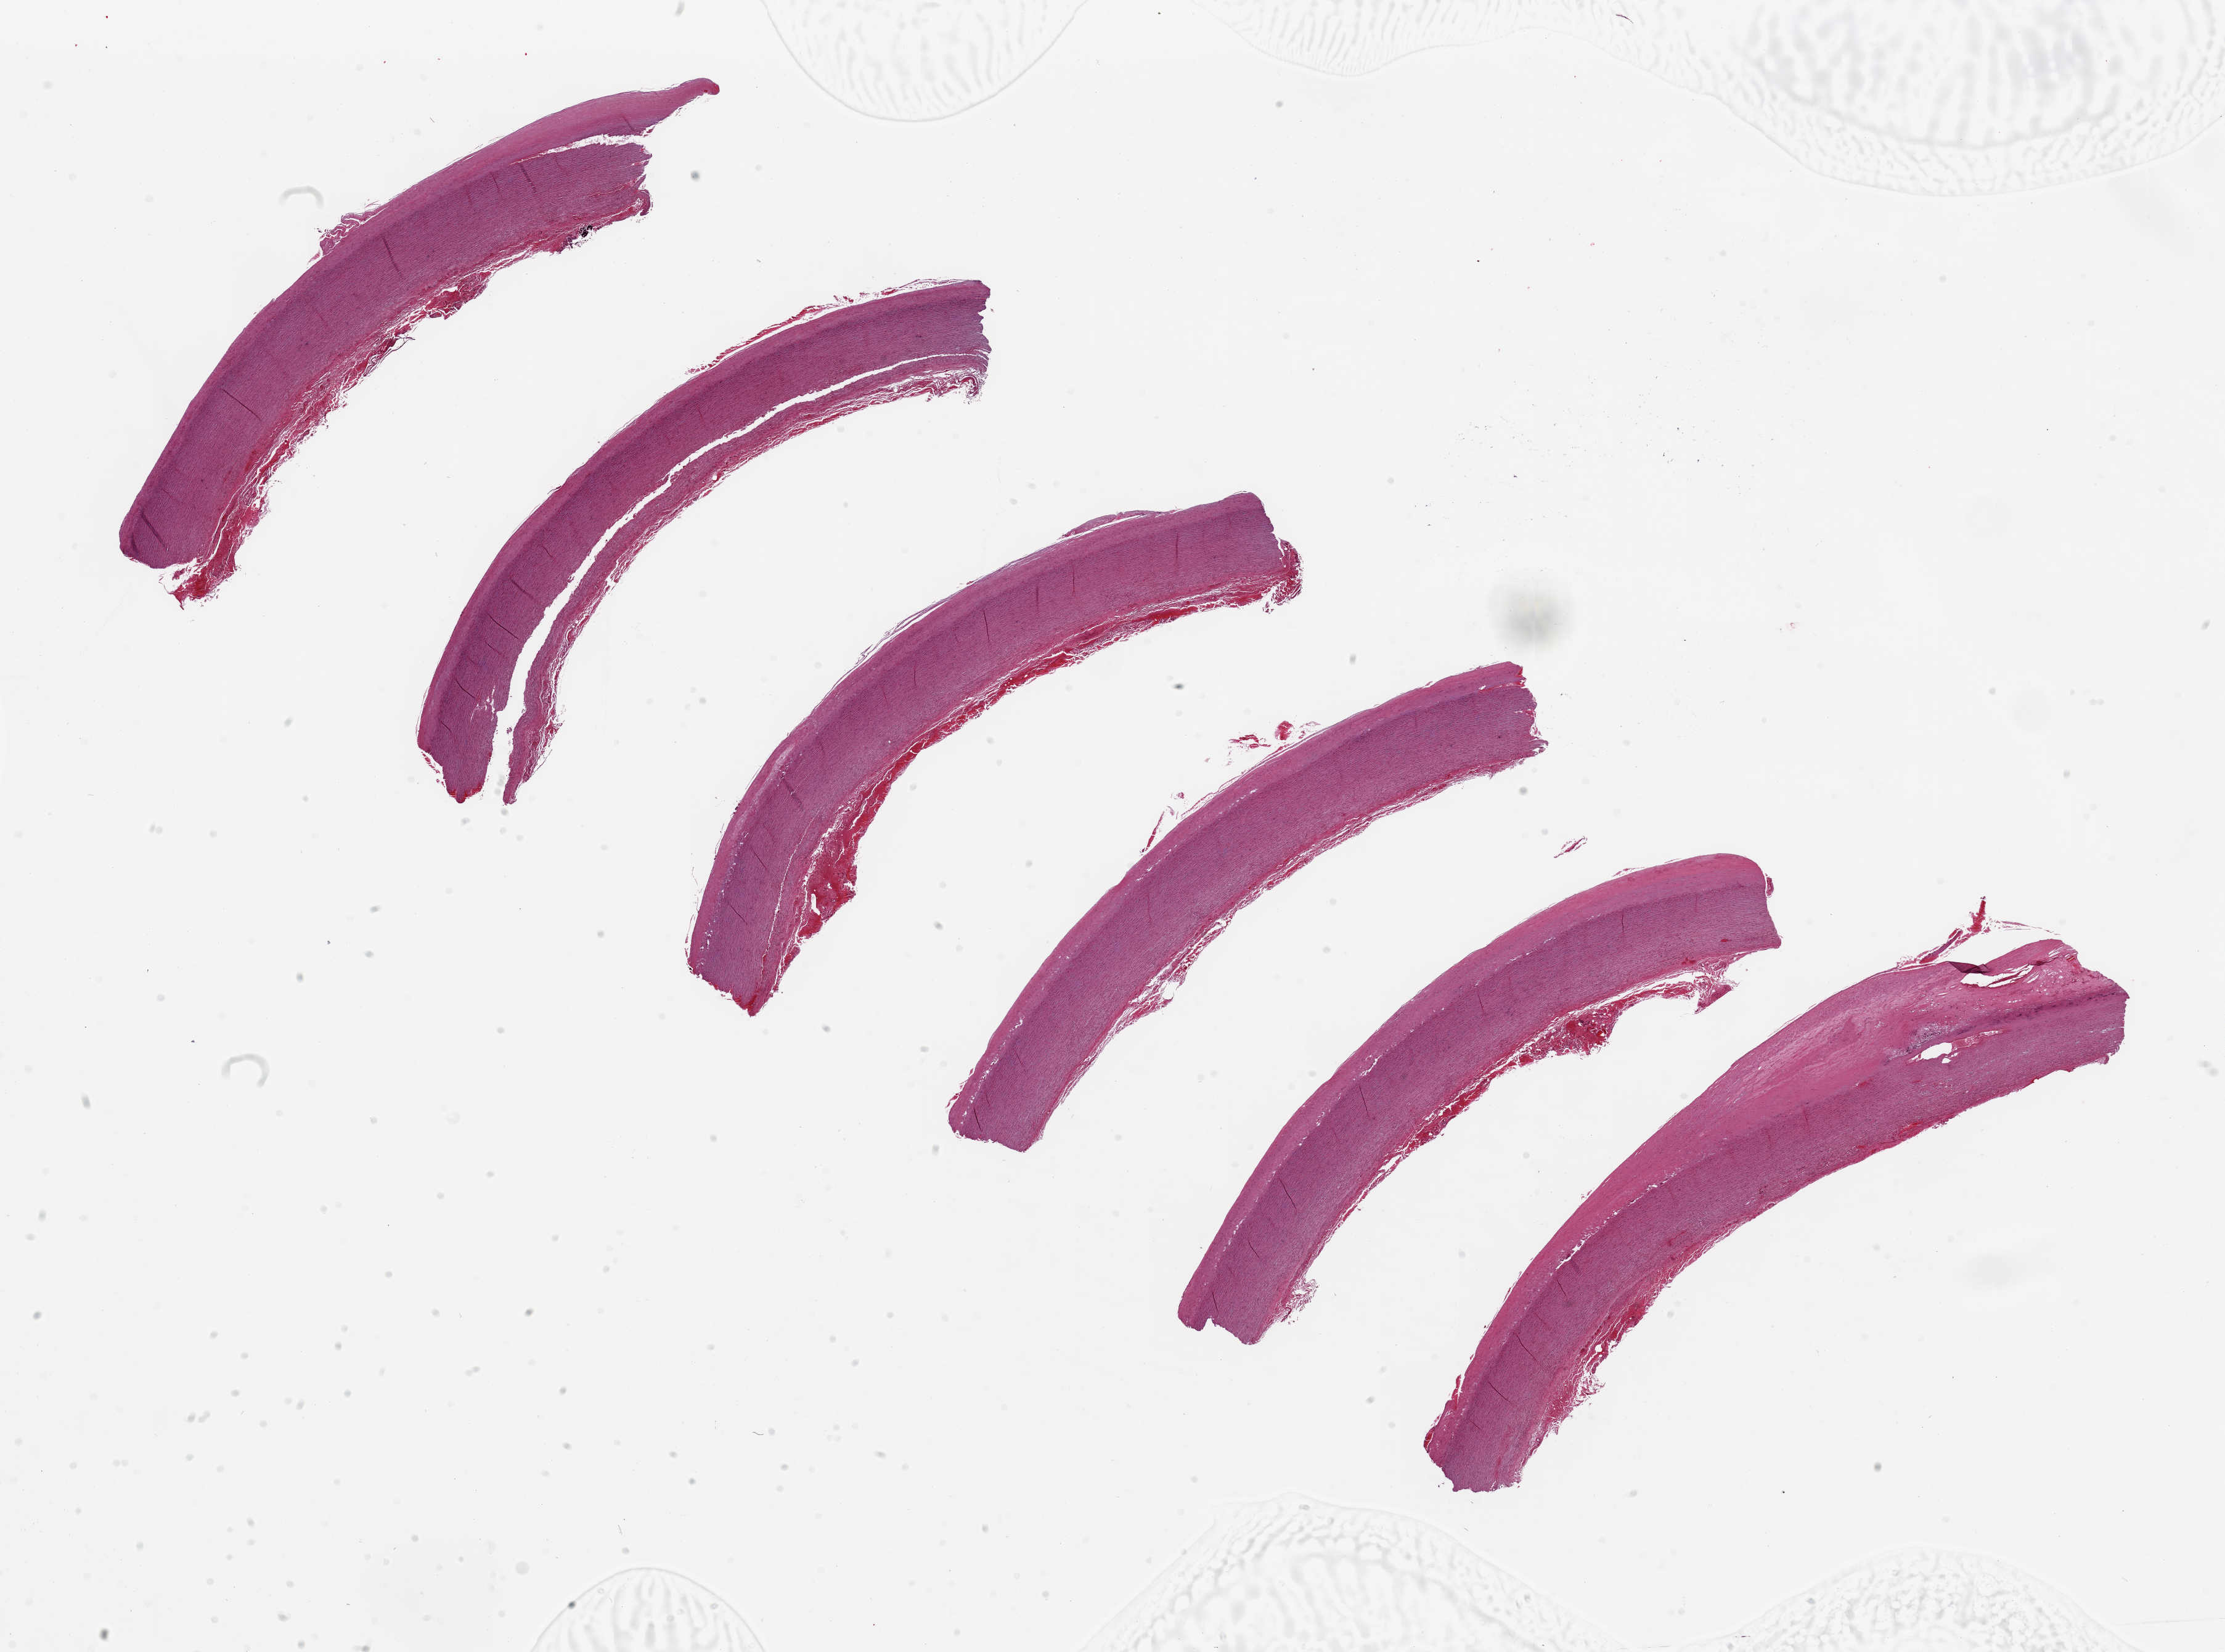
Digitized haematoxylin and eosin-stained section, brightfield, a low-resolution overview of the entire scanned area, about 28.5 x 21.2 mm, PAXgene-fixed paraffin-embedded (PFPE) section, sampled site (target tissue): aorta, donor tissue sample.
Reviewer comment on this tissue sample: 6 ~10x2mm pieces, some with up to 1mm thick atheromatous deposits.